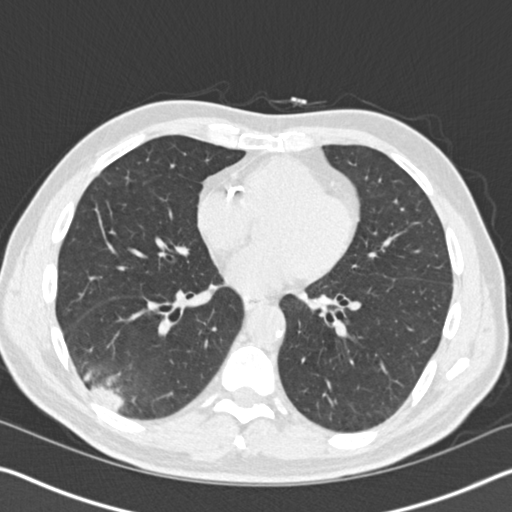
Axial slice from a low-dose chest CT screening exam. First (baseline) screen. Lung window (W 1500 / L -600 HU). Standard (soft-tissue) reconstruction kernel (B30f). Slice 91 of 161 in the series. Male participant, aged 61 years at enrolment.
Lesion marked by an expert reader, box from (x=52, y=333) to (x=160, y=425) px. The exam's reader record, not a measurement of the box and not confirmed to be the same lesion: non-calcified nodule or mass ≥4 mm, right lower lobe, 52 × 36 mm, spiculated (stellate) margins, soft tissue attenuation.